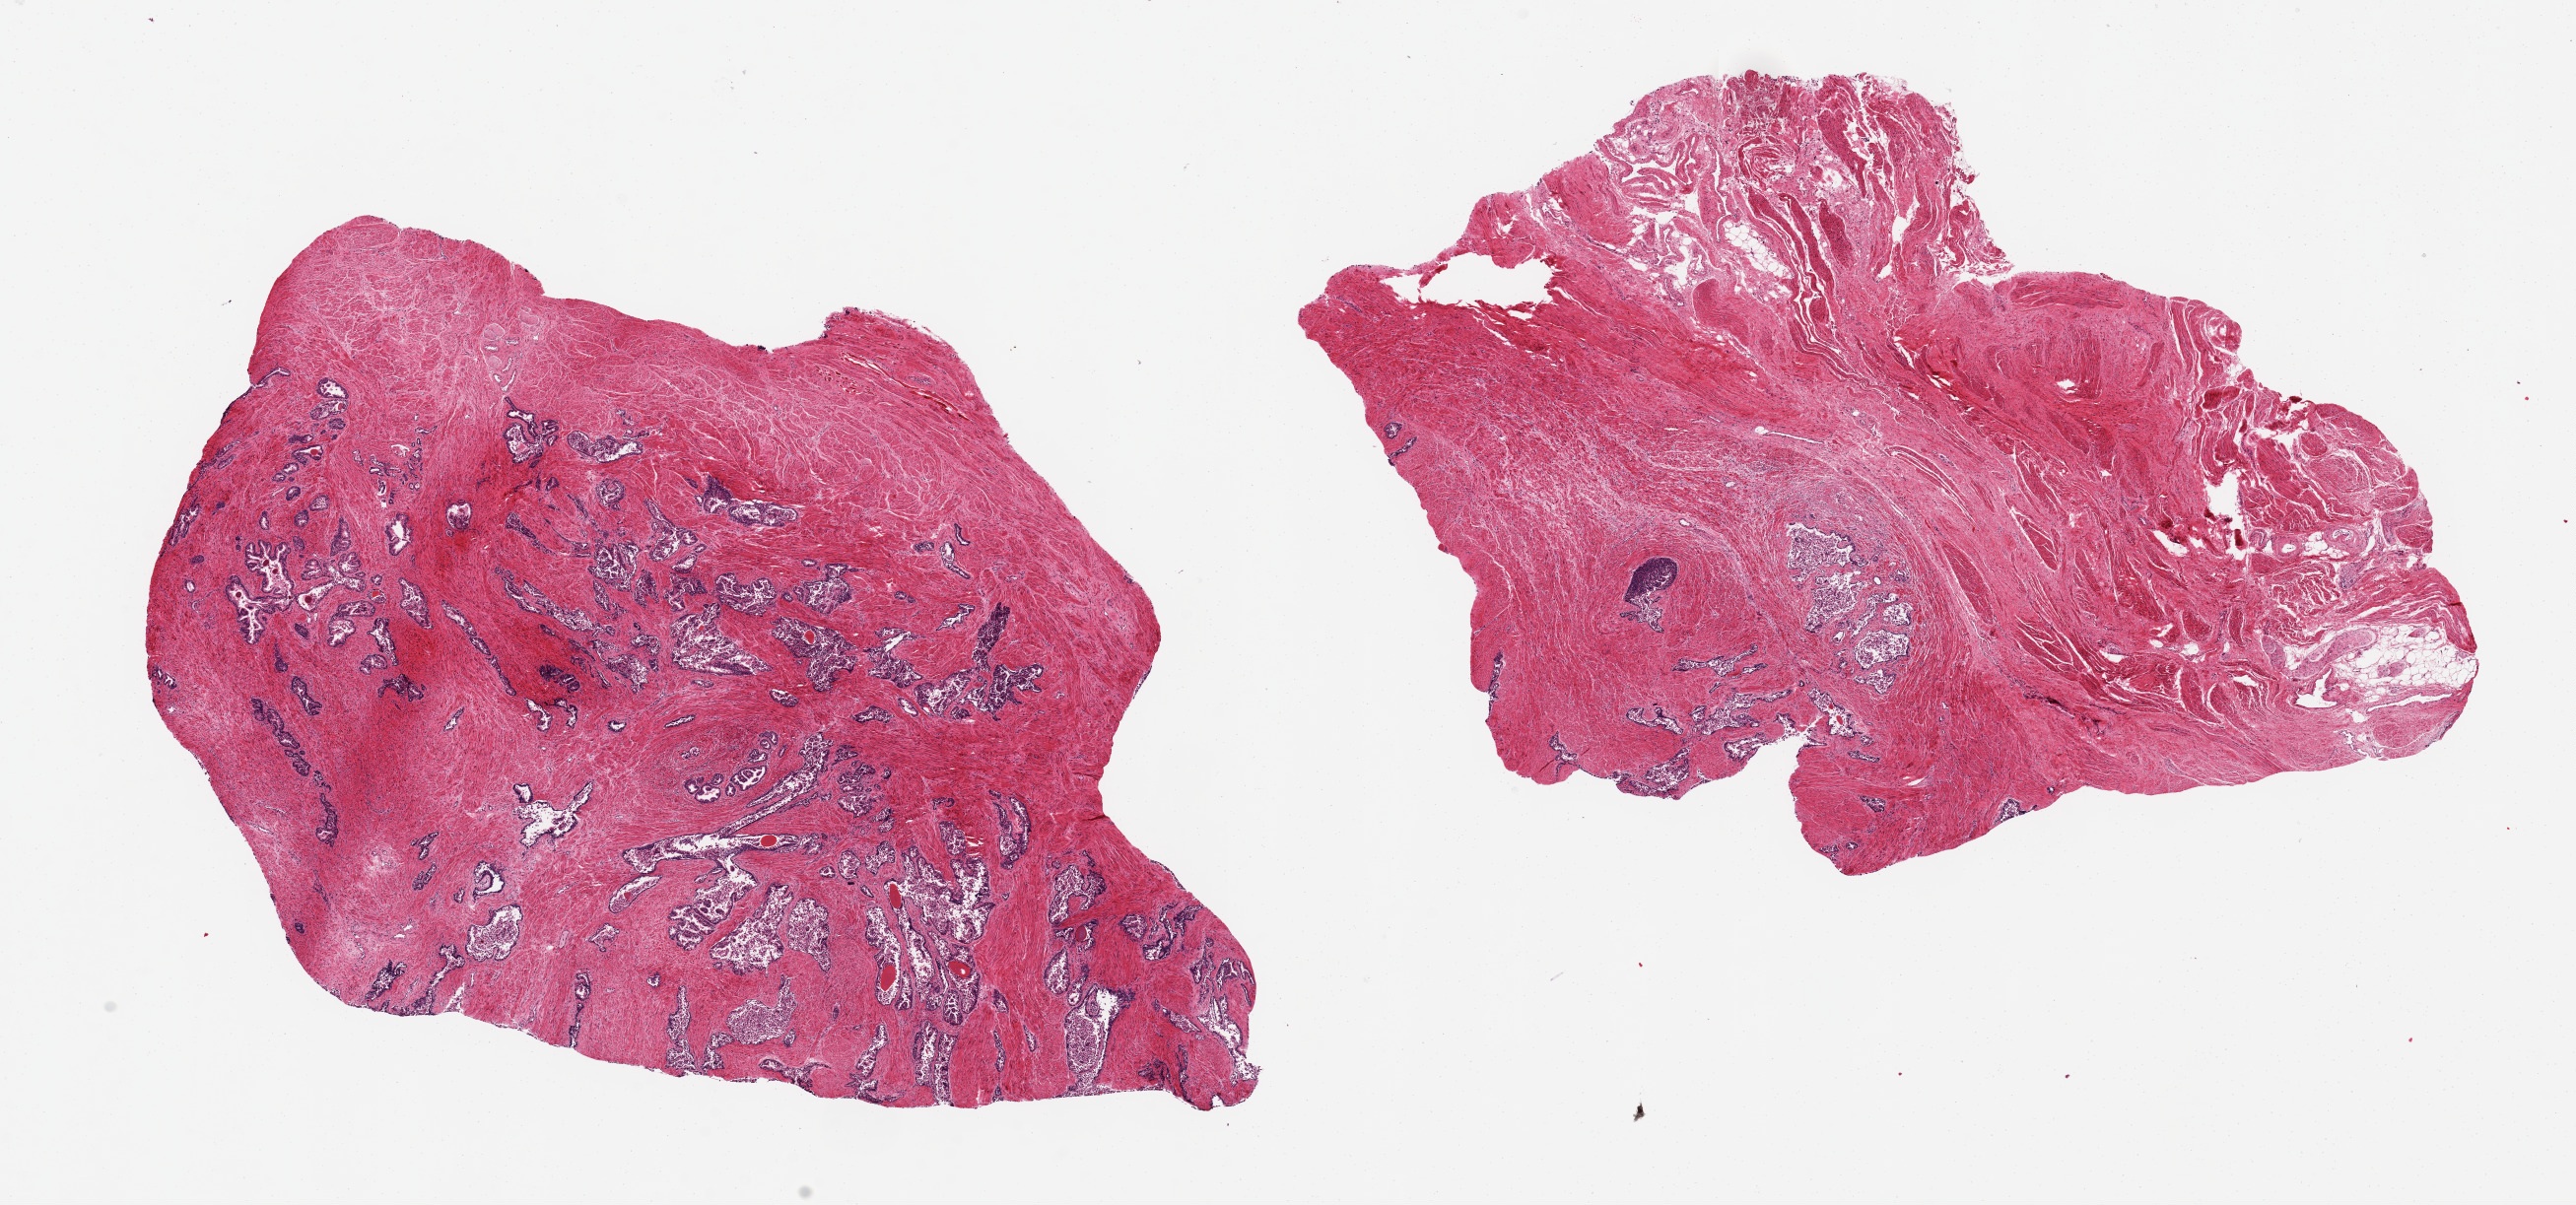
Digitized H&E-stained section, brightfield, shown as a low-resolution overview of the whole scanned area (about 20.7 x 9.7 mm), PAXgene-fixed, paraffin-embedded tissue, target tissue: prostate, tissue donor sample.
- pathologist's review note for this sample: 2 aliquots, ~10x6mm. Glands with moderate-marked mucosal autolysis. Glandular and stromal hyperplasia